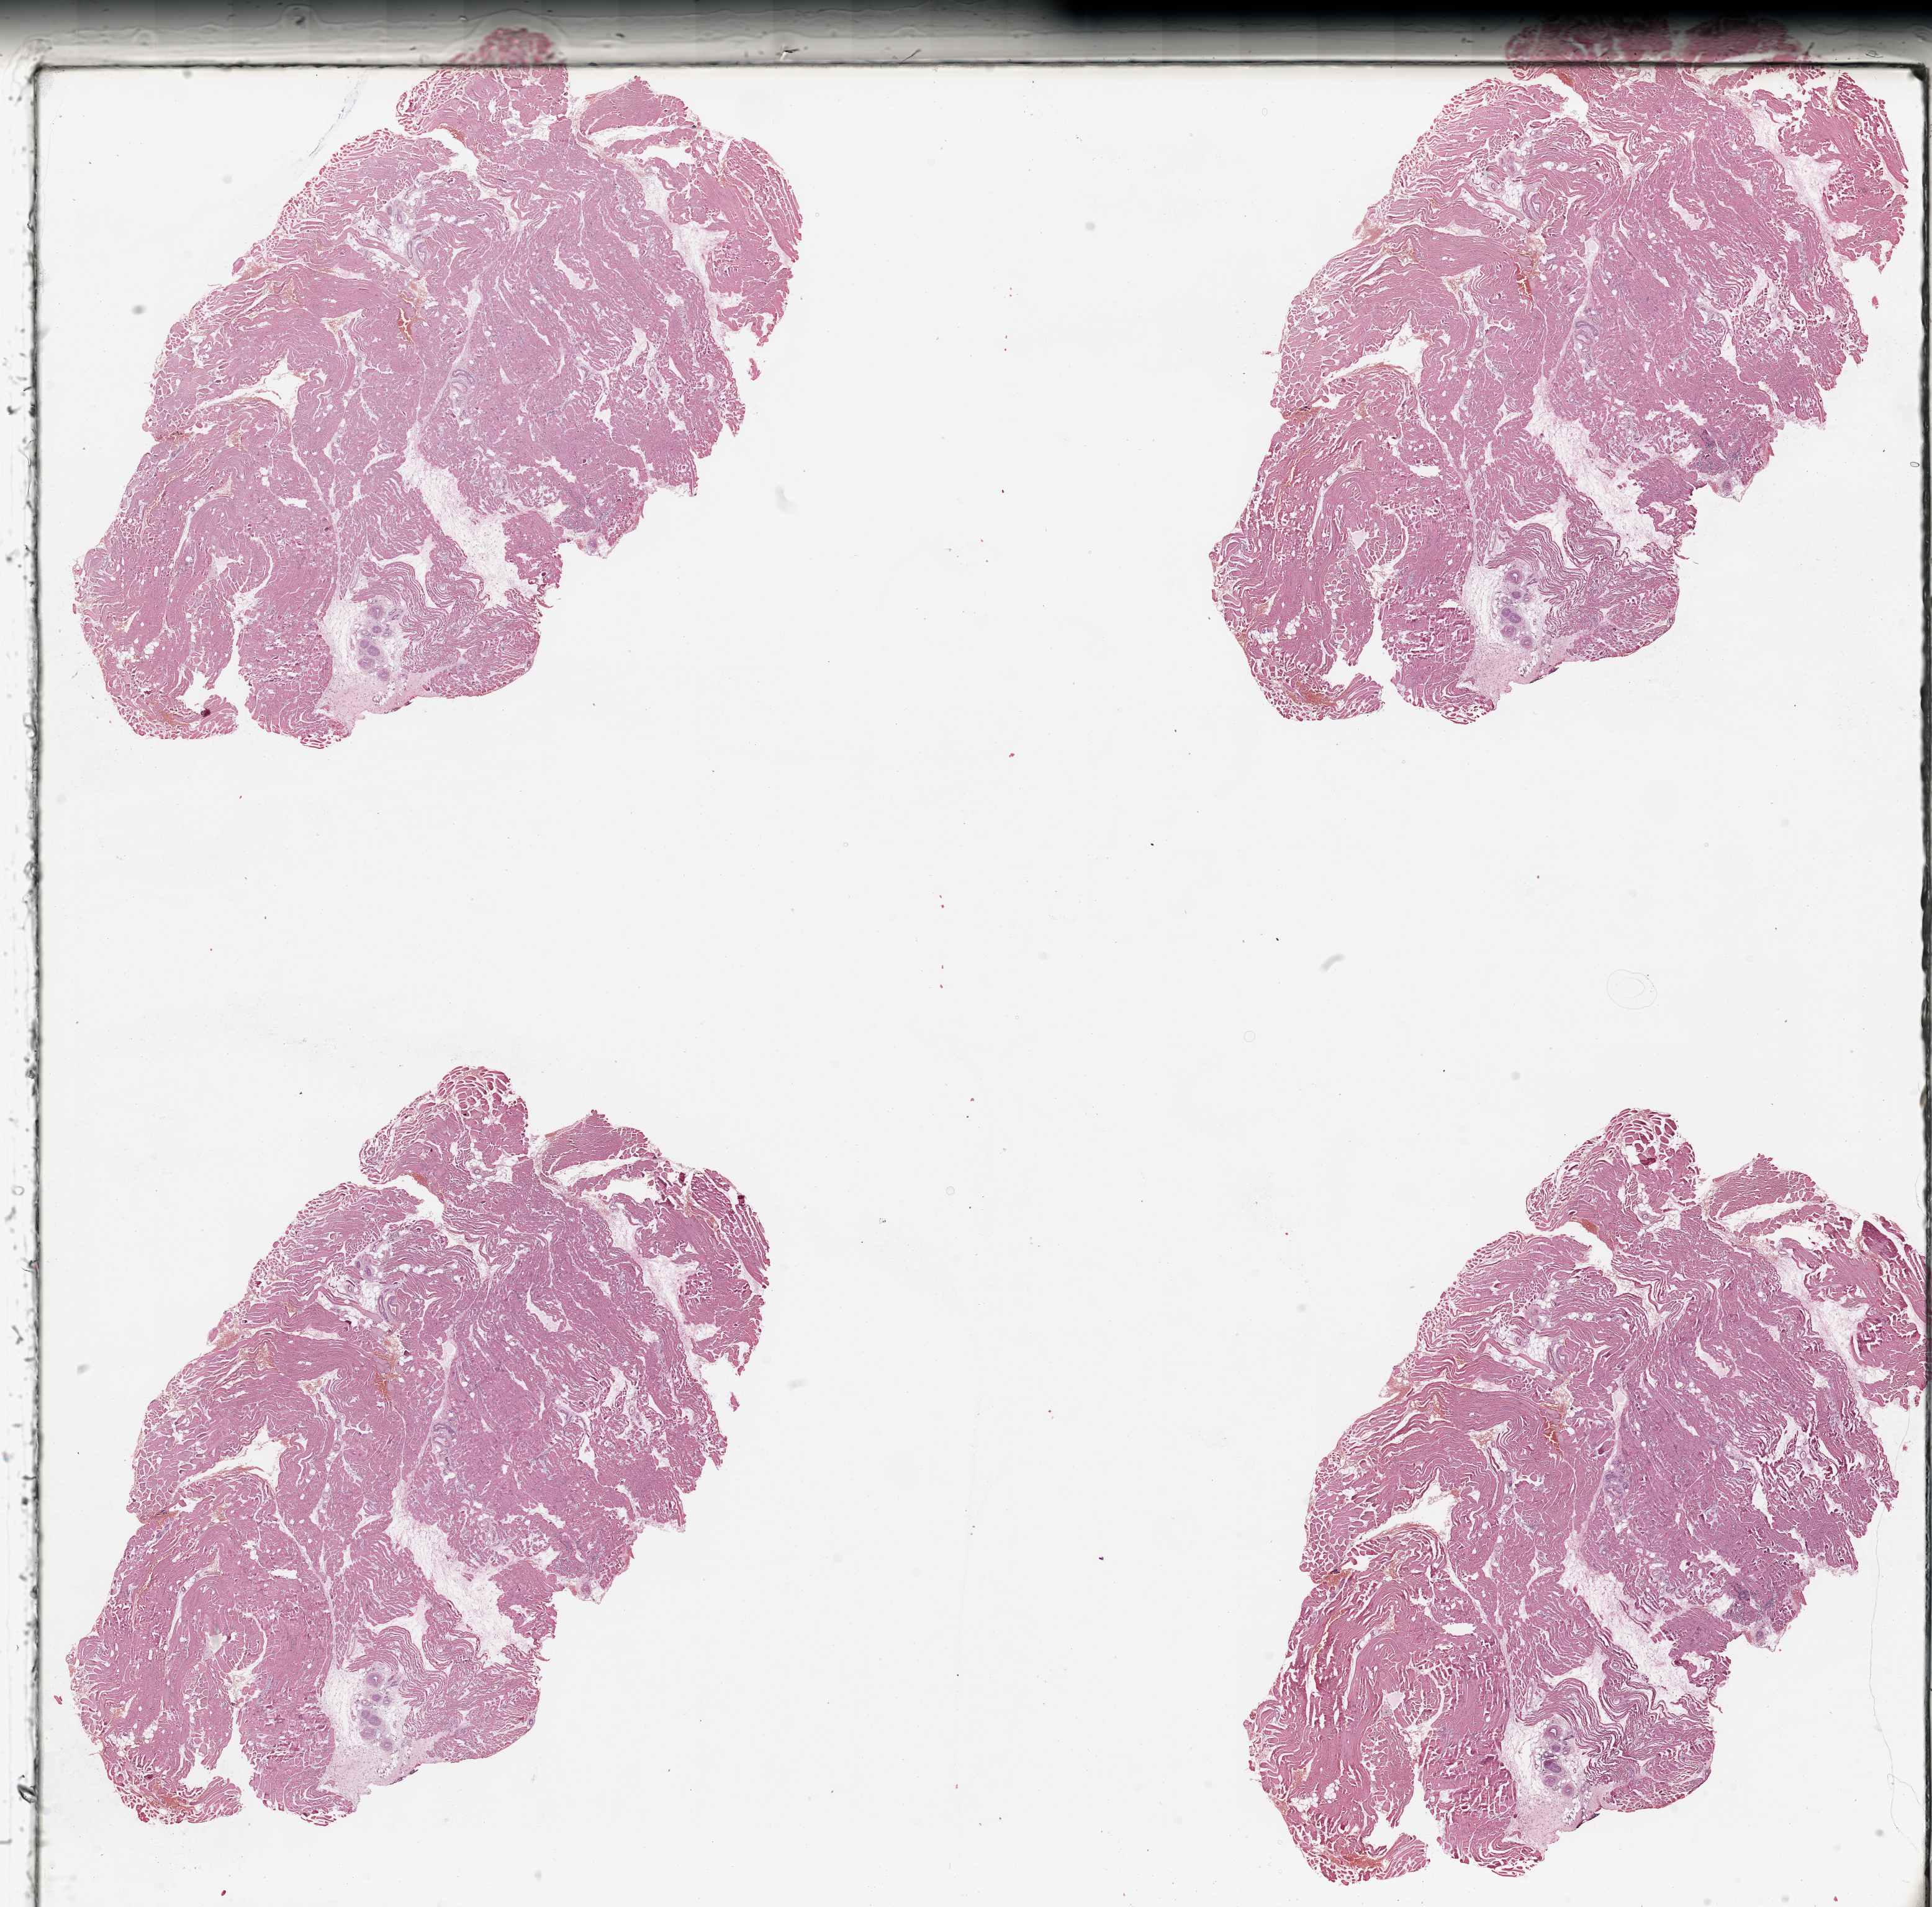
Whole-slide histology image, Hematoxylin and eosin (H&E) stained, whole scanned area (about 24.6 x 24.3 mm, slide scanned at 20x) shown as a low-resolution overview, normal (non-tumour) tissue sample. 52-year-old female patient.
This section: normal (non-tumour) tissue from the same patient. Patient diagnosis (cohort enrolment): sarcoma (site not recorded at cohort level).